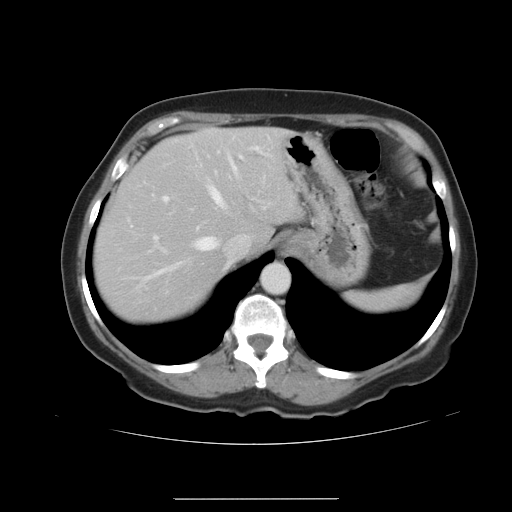
Contrast-enhanced abdominal CT, one axial slice; position 30 of 41 along the scan axis; soft-tissue window (W 400 / L 40 HU); 5 mm slice thickness; 512 × 512 image matrix, field of view 381 × 381 mm. Female patient, age 63 years. From the clinical record (not read from this slice): diagnosis: colorectal cancer liver metastases, imaged before liver resection; multiple liver metastases: yes; largest metastasis: 1.5 cm.
Annotated regions visible in this slice (outlined manually by an expert reader):
- hepatic veins: bounding box [x1, y1, x2, y2] px = [130, 141, 236, 286]
- liver: [96, 128, 301, 320]
- planned liver remnant (the part of the liver to remain after resection): [96, 128, 301, 320]
- portal vein (with intrahepatic branches): [154, 154, 244, 239]